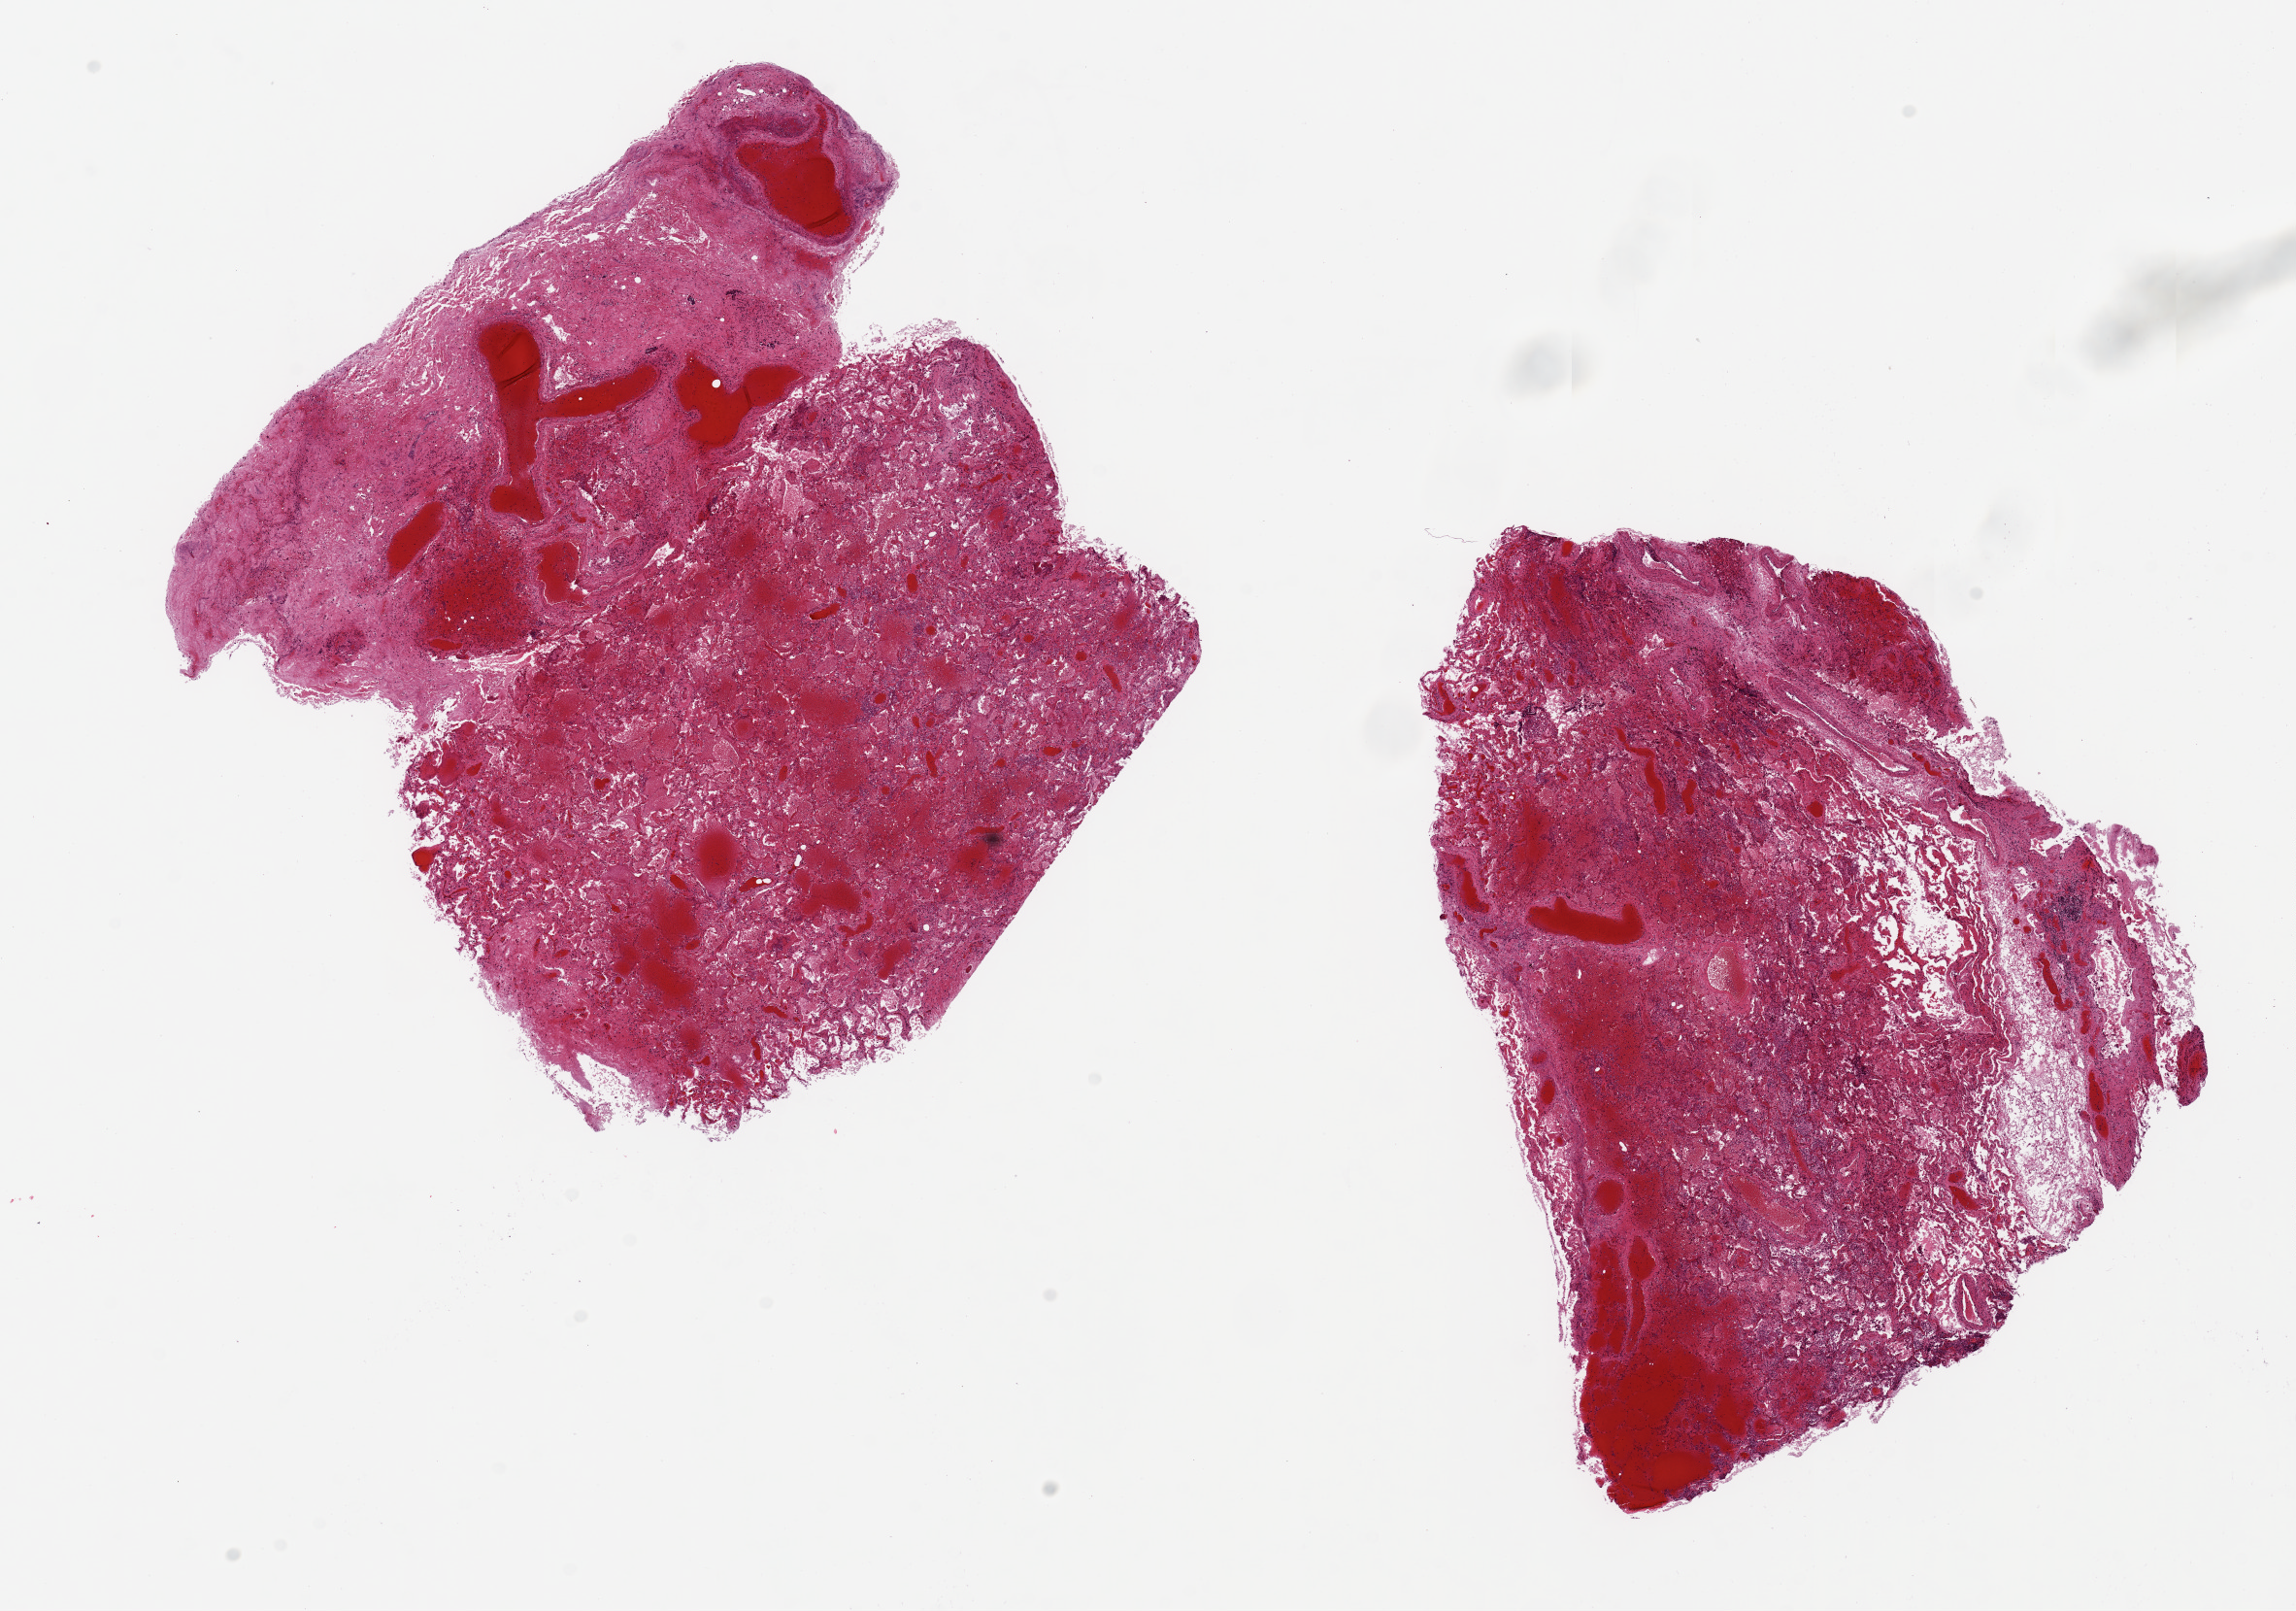
Whole-slide image, hematoxylin and eosin (H&E) stain, a low-resolution overview of the entire scanned area, about 18.7 x 13.1 mm (acquisition: 20x scan). PAXgene-fixed paraffin-embedded (PFPE) section. Sampled site (target tissue): lung. Tissue donor sample. Donor: female.
Pathologist's review note for this sample: 2 pieces ~7x6mm. Marked hemorrhage with chronic pneumonitis/edema/congestion.